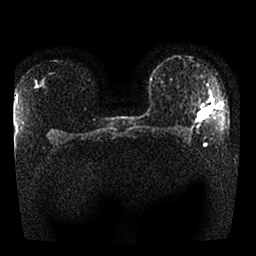
Breast MRI, one axial slice; position 17 of 25 along the scan axis; diffusion-weighted series; image 2 of 4 stored at this slice position (different b-values; order by instance number); 1.5 T; 4 mm slice thickness; 256 × 256 image matrix. Female patient.
Annotated regions visible in this slice (expert manual segmentation):
- tumour on diffusion-weighted imaging: bounding box (x1, y1, x2, y2) in pixels: (198, 109, 208, 120)